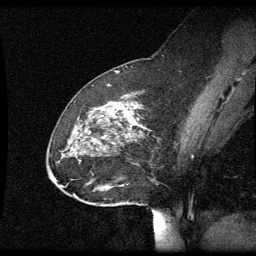
Breast MRI (dynamic contrast-enhanced), one sagittal slice; position 23 of 60 along the scan axis; dynamic contrast-enhanced series, image 2 of 3 at this slice position (ordered by acquisition); 1.5 T; TE 4.2 ms, TR 8.9 ms; 2 mm slice thickness; 256 × 256 image matrix, field of view 200 × 200 mm. Patient: female, 49 years. From the clinical record (not read from this slice): setting: breast cancer imaged before/during neoadjuvant chemotherapy; receptor status: HR-positive, HER2-negative.
Structures marked on this image (semi-automatically segmented with operator editing):
- analysis volume of interest (the breast-tissue region the enhancement analysis was run in; not a lesion): bounding box <48,94,144,205> (left, top, right, bottom; pixels)
- tumour enhancement mask (voxels above the 70 % enhancement threshold inside the analysis volume of interest): <117,104,138,127>